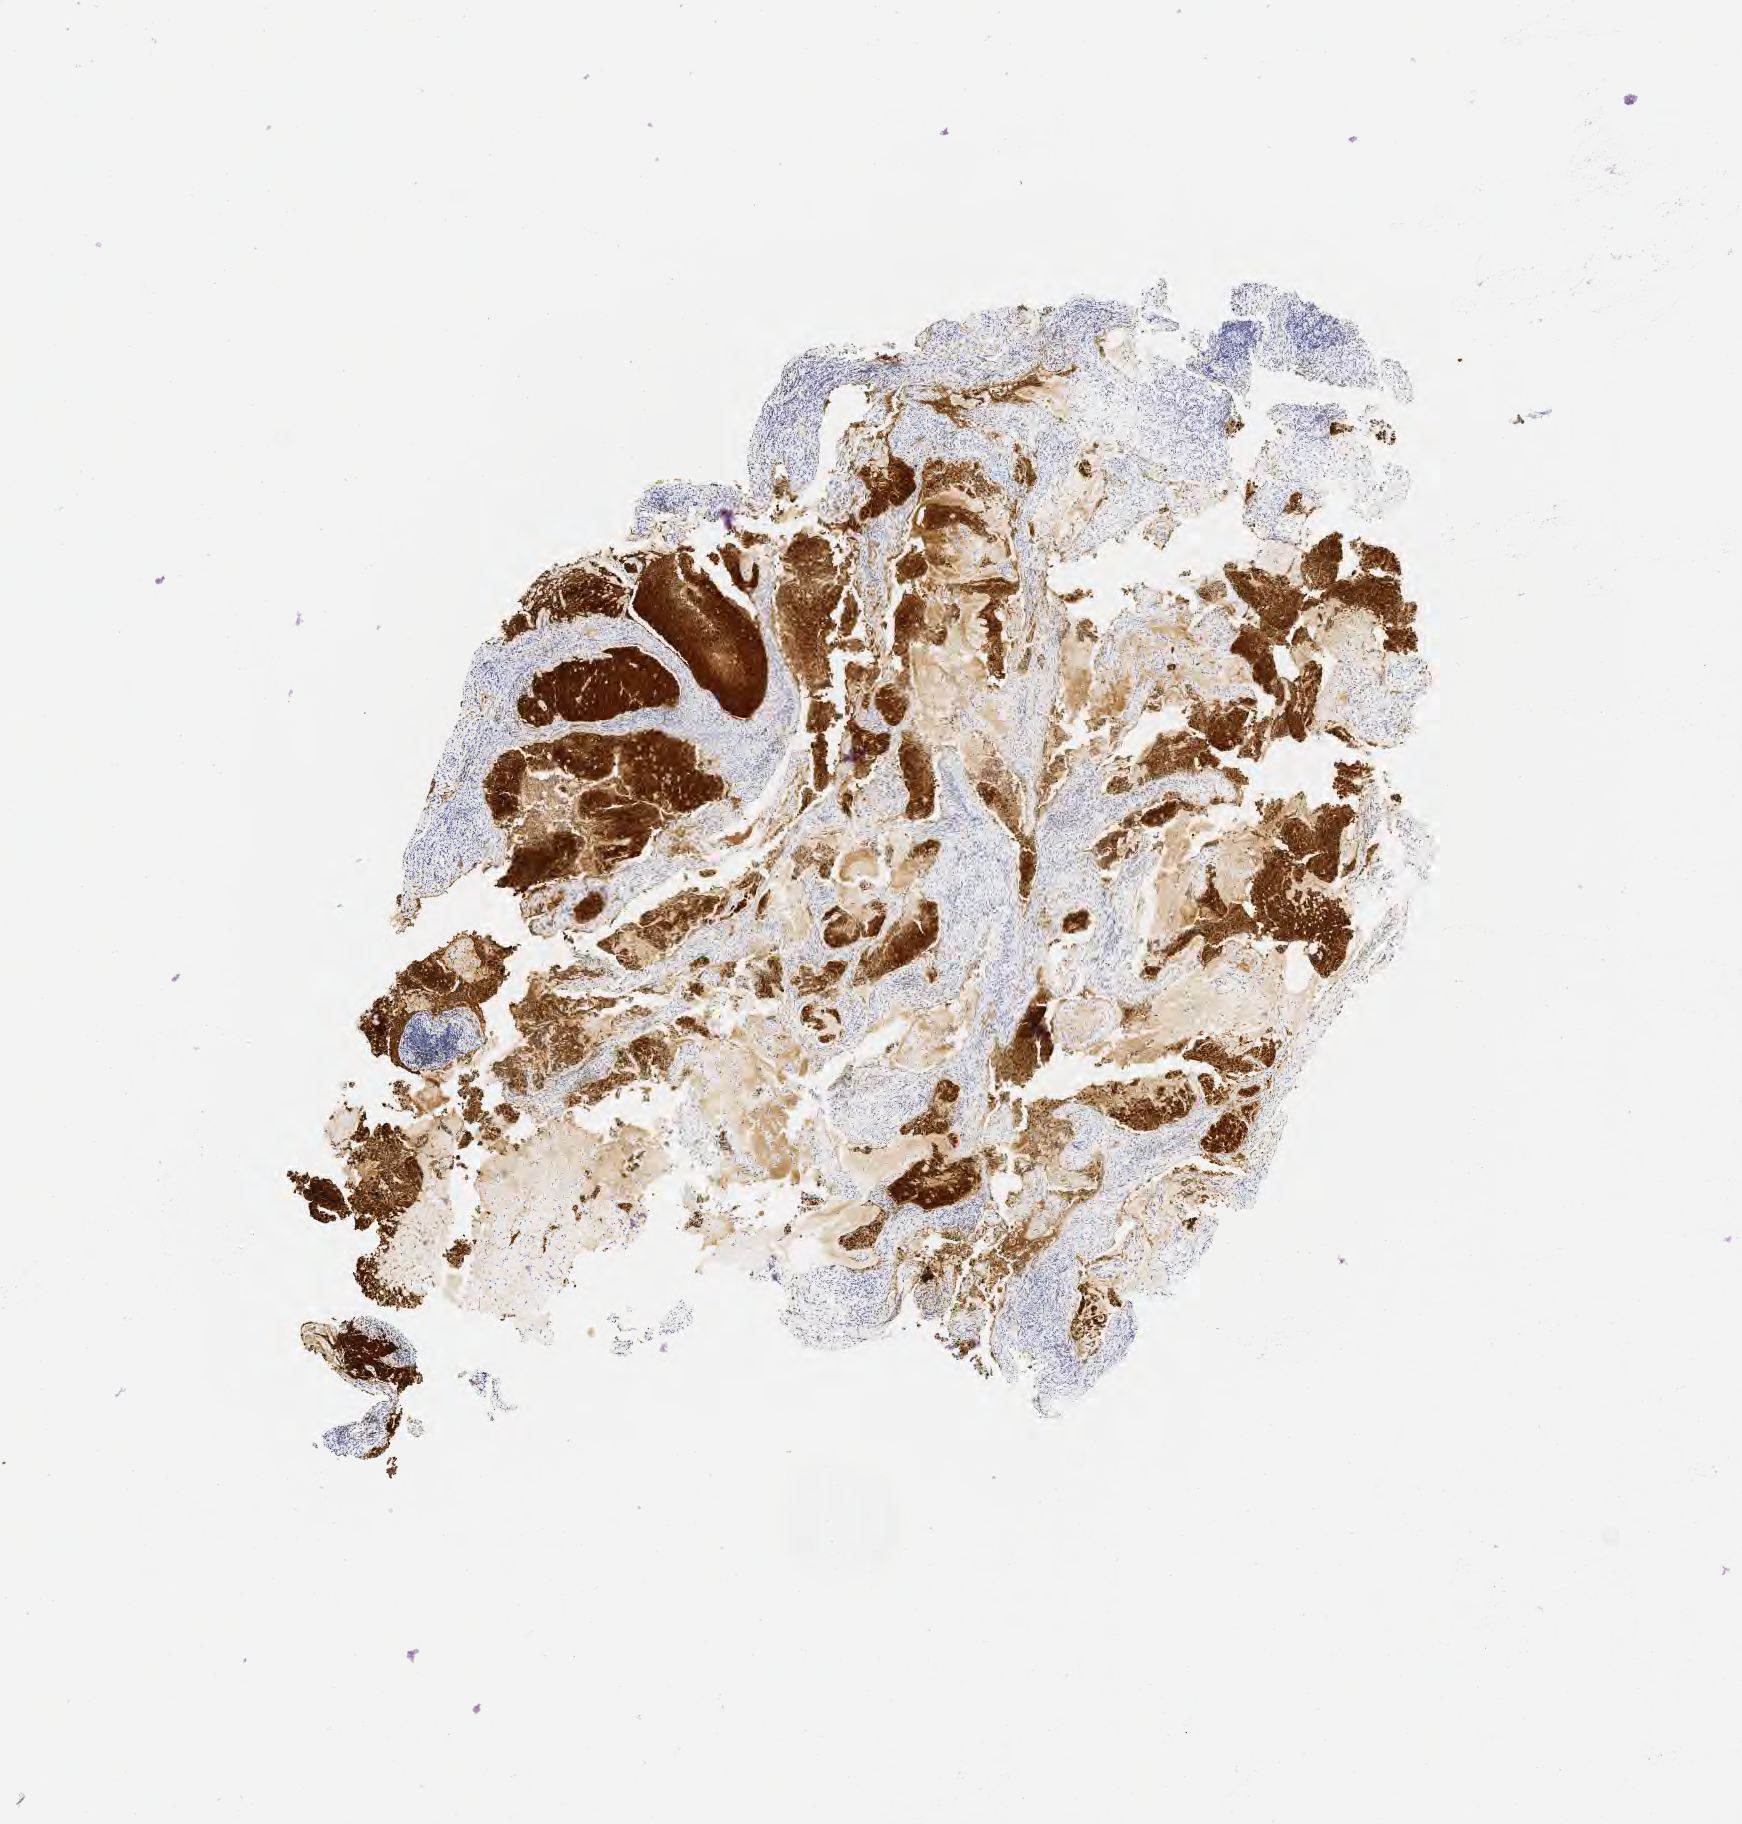
Immunohistochemistry (IHC) whole-slide image stained for p16 (p16INK4a), whole scanned area (about 7.0 x 7.4 mm) shown as a low-resolution overview; specimen: tumor tissue; anatomic site: cervix. Patient: female, 43 years old.
Histologic diagnosis: Adenocarcinoma, NOS.